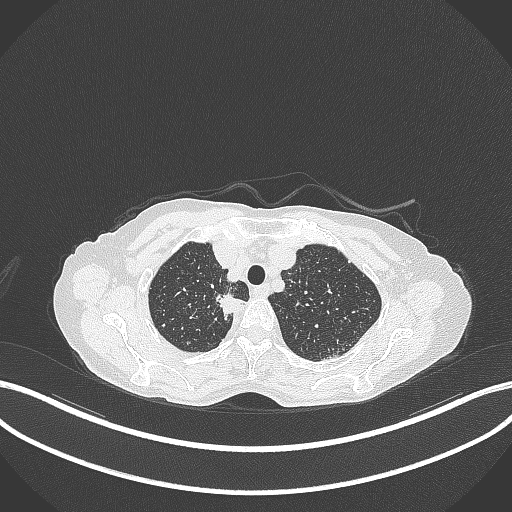
Chest CT, one axial slice. Slice 314 of 403 in the series (ordered by position). Reconstruction kernel B70f. Lung window (W 1500 / L -600 HU). 1 mm slice thickness. 512 × 512 image matrix, field of view 400 × 400 mm. Patient: female, 75 years. Case-level facts recorded for this patient, not image findings: clinical TNM (as recorded): T1c N1 M1.
Outlined on this slice (bounding box drawn by a radiologist):
- lung tumour (recorded histology: adenocarcinoma): bounding box [x1, y1, x2, y2] px = [212, 290, 250, 321]